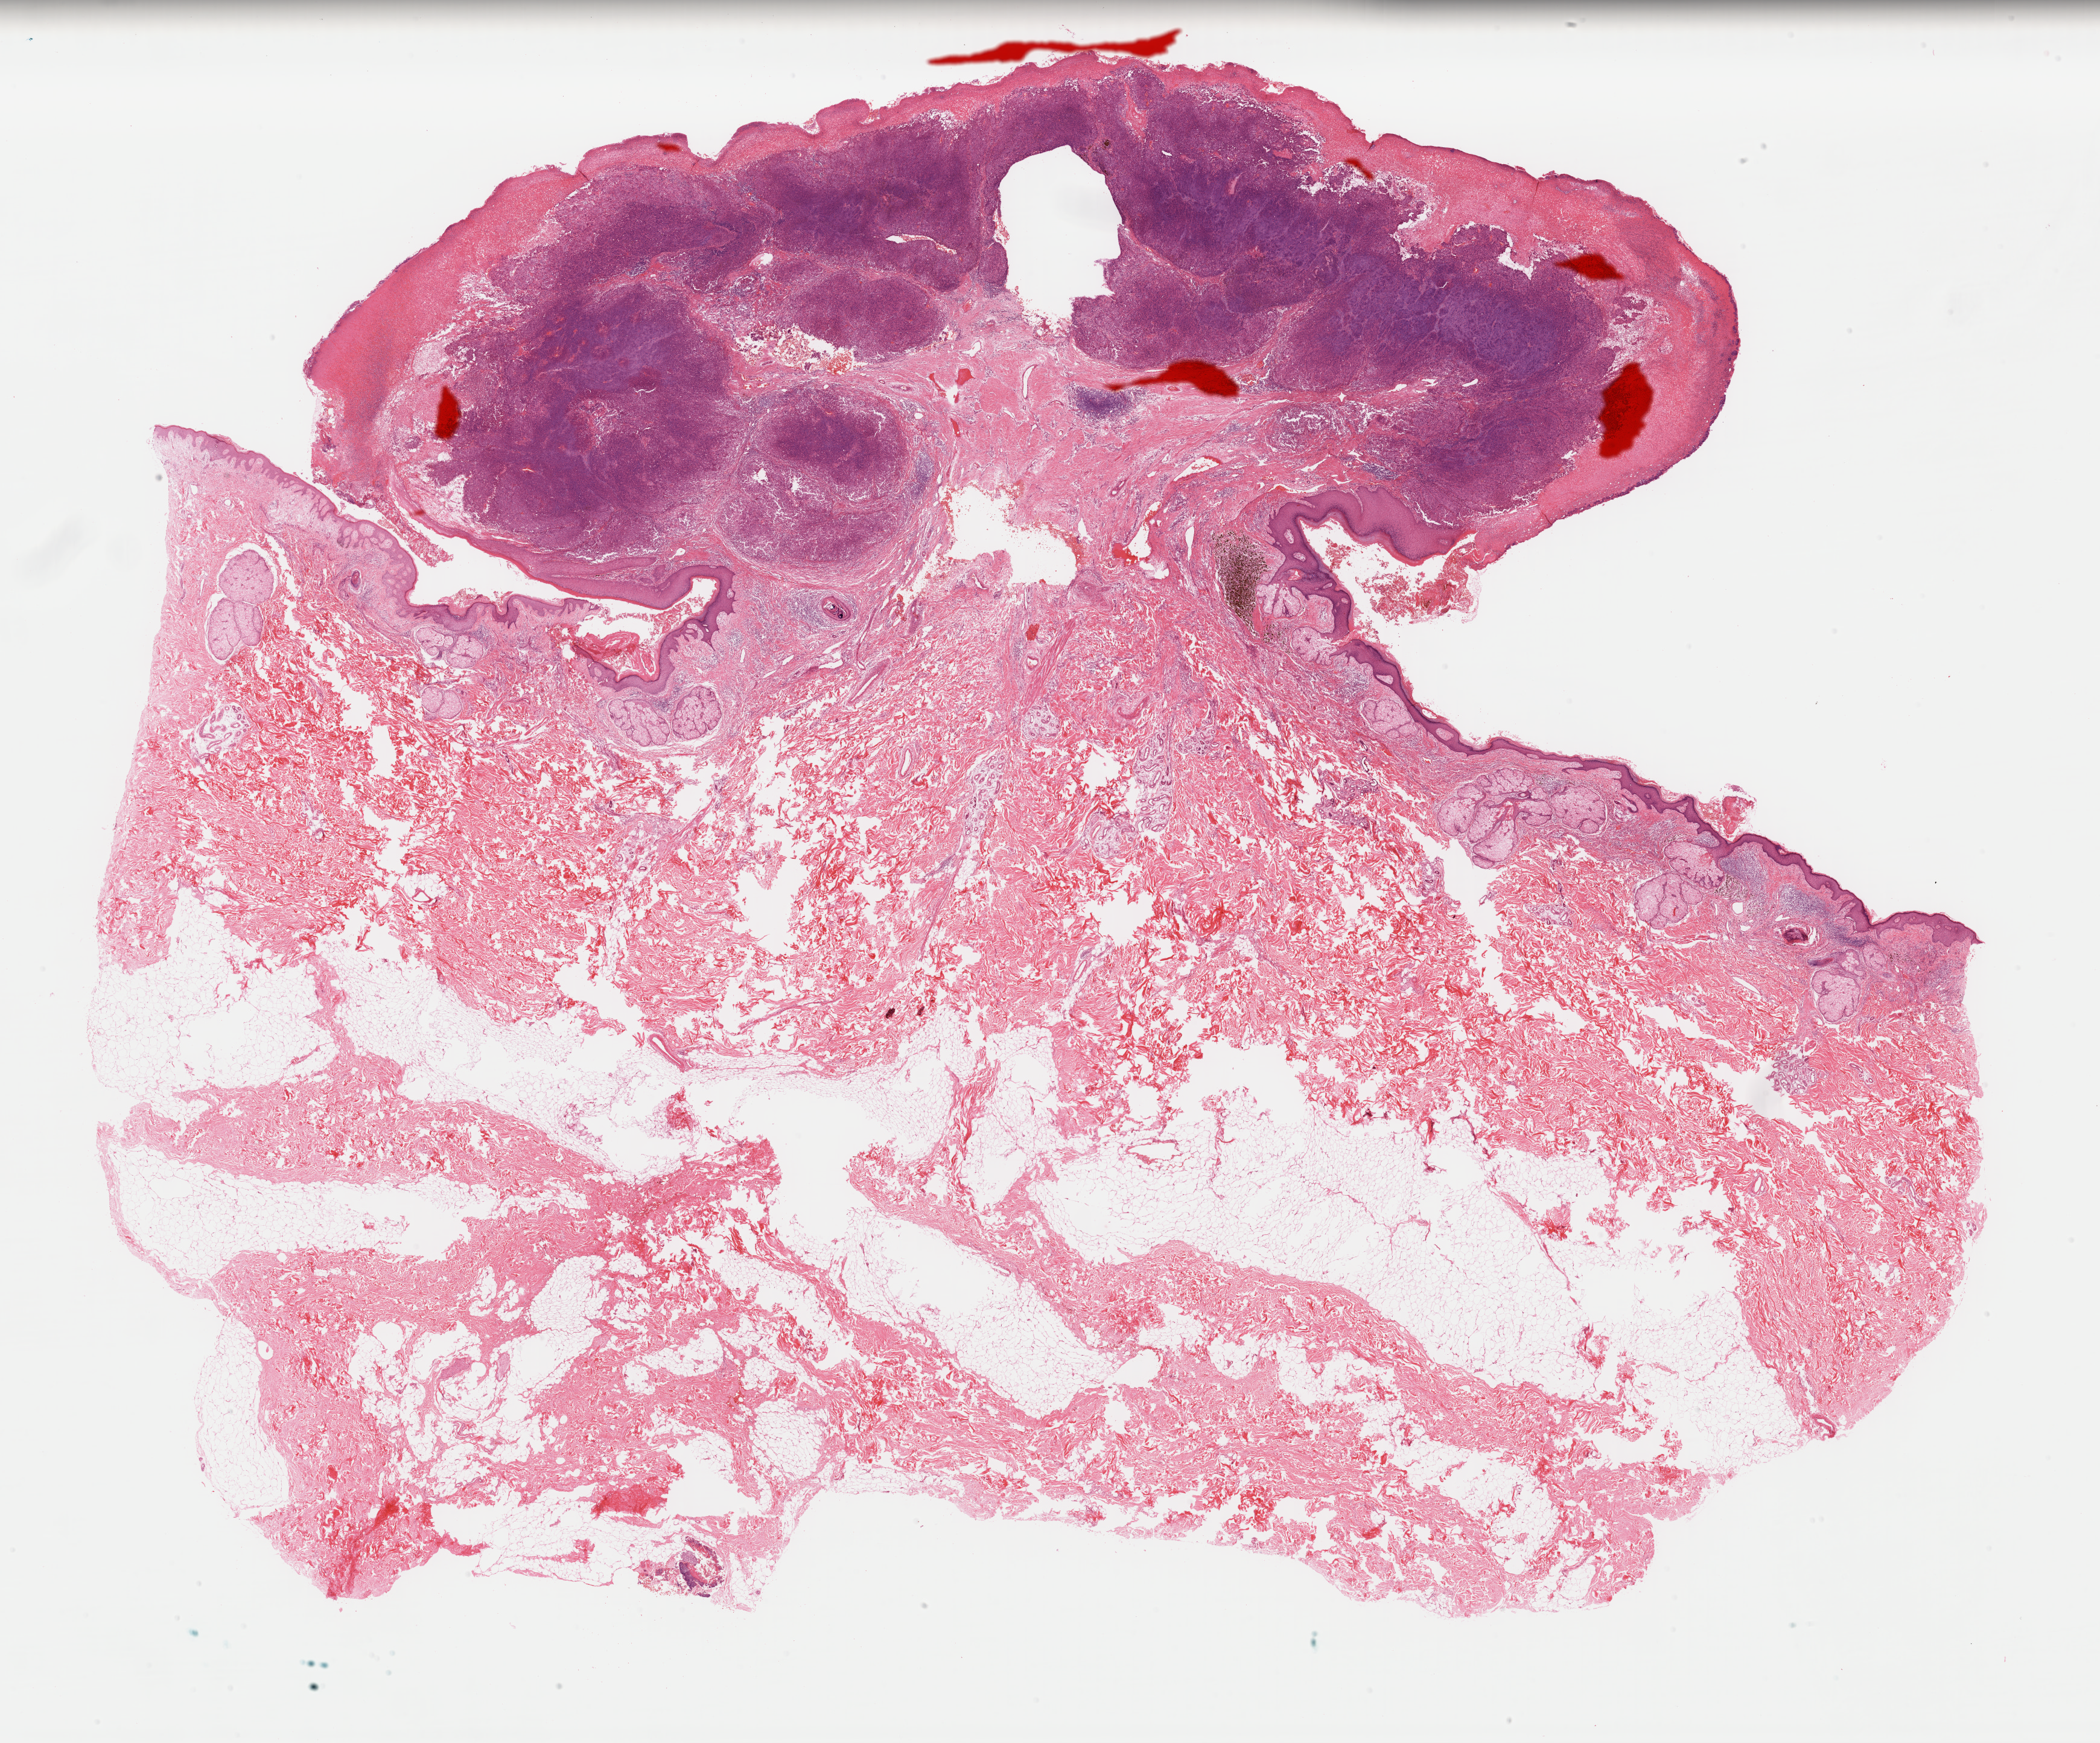
Digitized H&E-stained tissue section (whole slide), shown as a low-resolution overview of the whole scanned area (about 27.5 x 22.8 mm, slide scanned at 40x). FFPE section. Primary tumour sample from the skin. Patient: male, age at initial diagnosis 83 years.
Histologic diagnosis: Nodular melanoma.